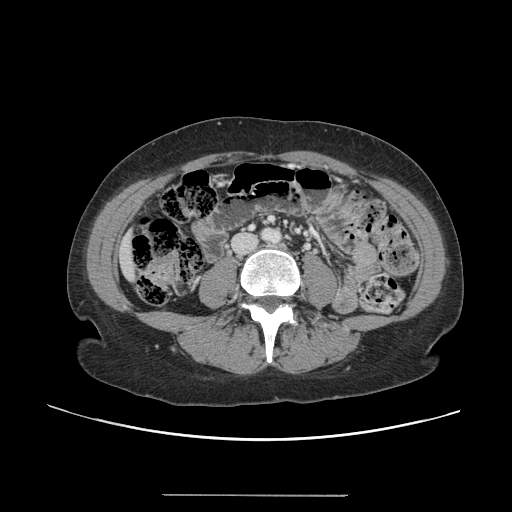
Contrast-enhanced abdominal CT, one axial slice; position 15 of 144 along the scan axis; intravenous contrast given; soft-tissue window (W 400 / L 40 HU); 512 × 512 image matrix, field of view 380 × 380 mm. Female patient, age 53 years. Case-level facts recorded for this patient, not image findings: diagnosis: colorectal cancer liver metastases, imaged before liver resection; multiple liver metastases: yes; largest metastasis: 1.1 cm; disease in both lobes: no.
Outlined on this slice (outlined manually by an expert reader):
- liver: bounding box [x1, y1, x2, y2] px = [119, 234, 136, 280]
- planned liver remnant (the part of the liver to remain after resection): [118, 234, 136, 282]